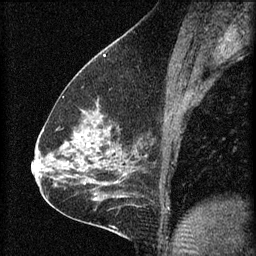
Breast MRI (dynamic contrast-enhanced), one sagittal slice; position 36 of 60 along the scan axis; 3 images stored at this slice position (order not interpretable as contrast timing); 1.5 T; TE 4.2 ms, TR 8.2 ms; 2 mm slice thickness; 256 × 256 image matrix, field of view 180 × 180 mm. Patient: female, 59 years.
Annotated regions visible in this slice (semi-automatically segmented with operator editing):
- analysis volume of interest (the breast-tissue region the enhancement analysis was run in; not a lesion): box from (x=61, y=104) to (x=134, y=161) px
- tumour enhancement mask (voxels above the 70 % enhancement threshold inside the analysis volume of interest): (x=75, y=104)–(x=112, y=149)